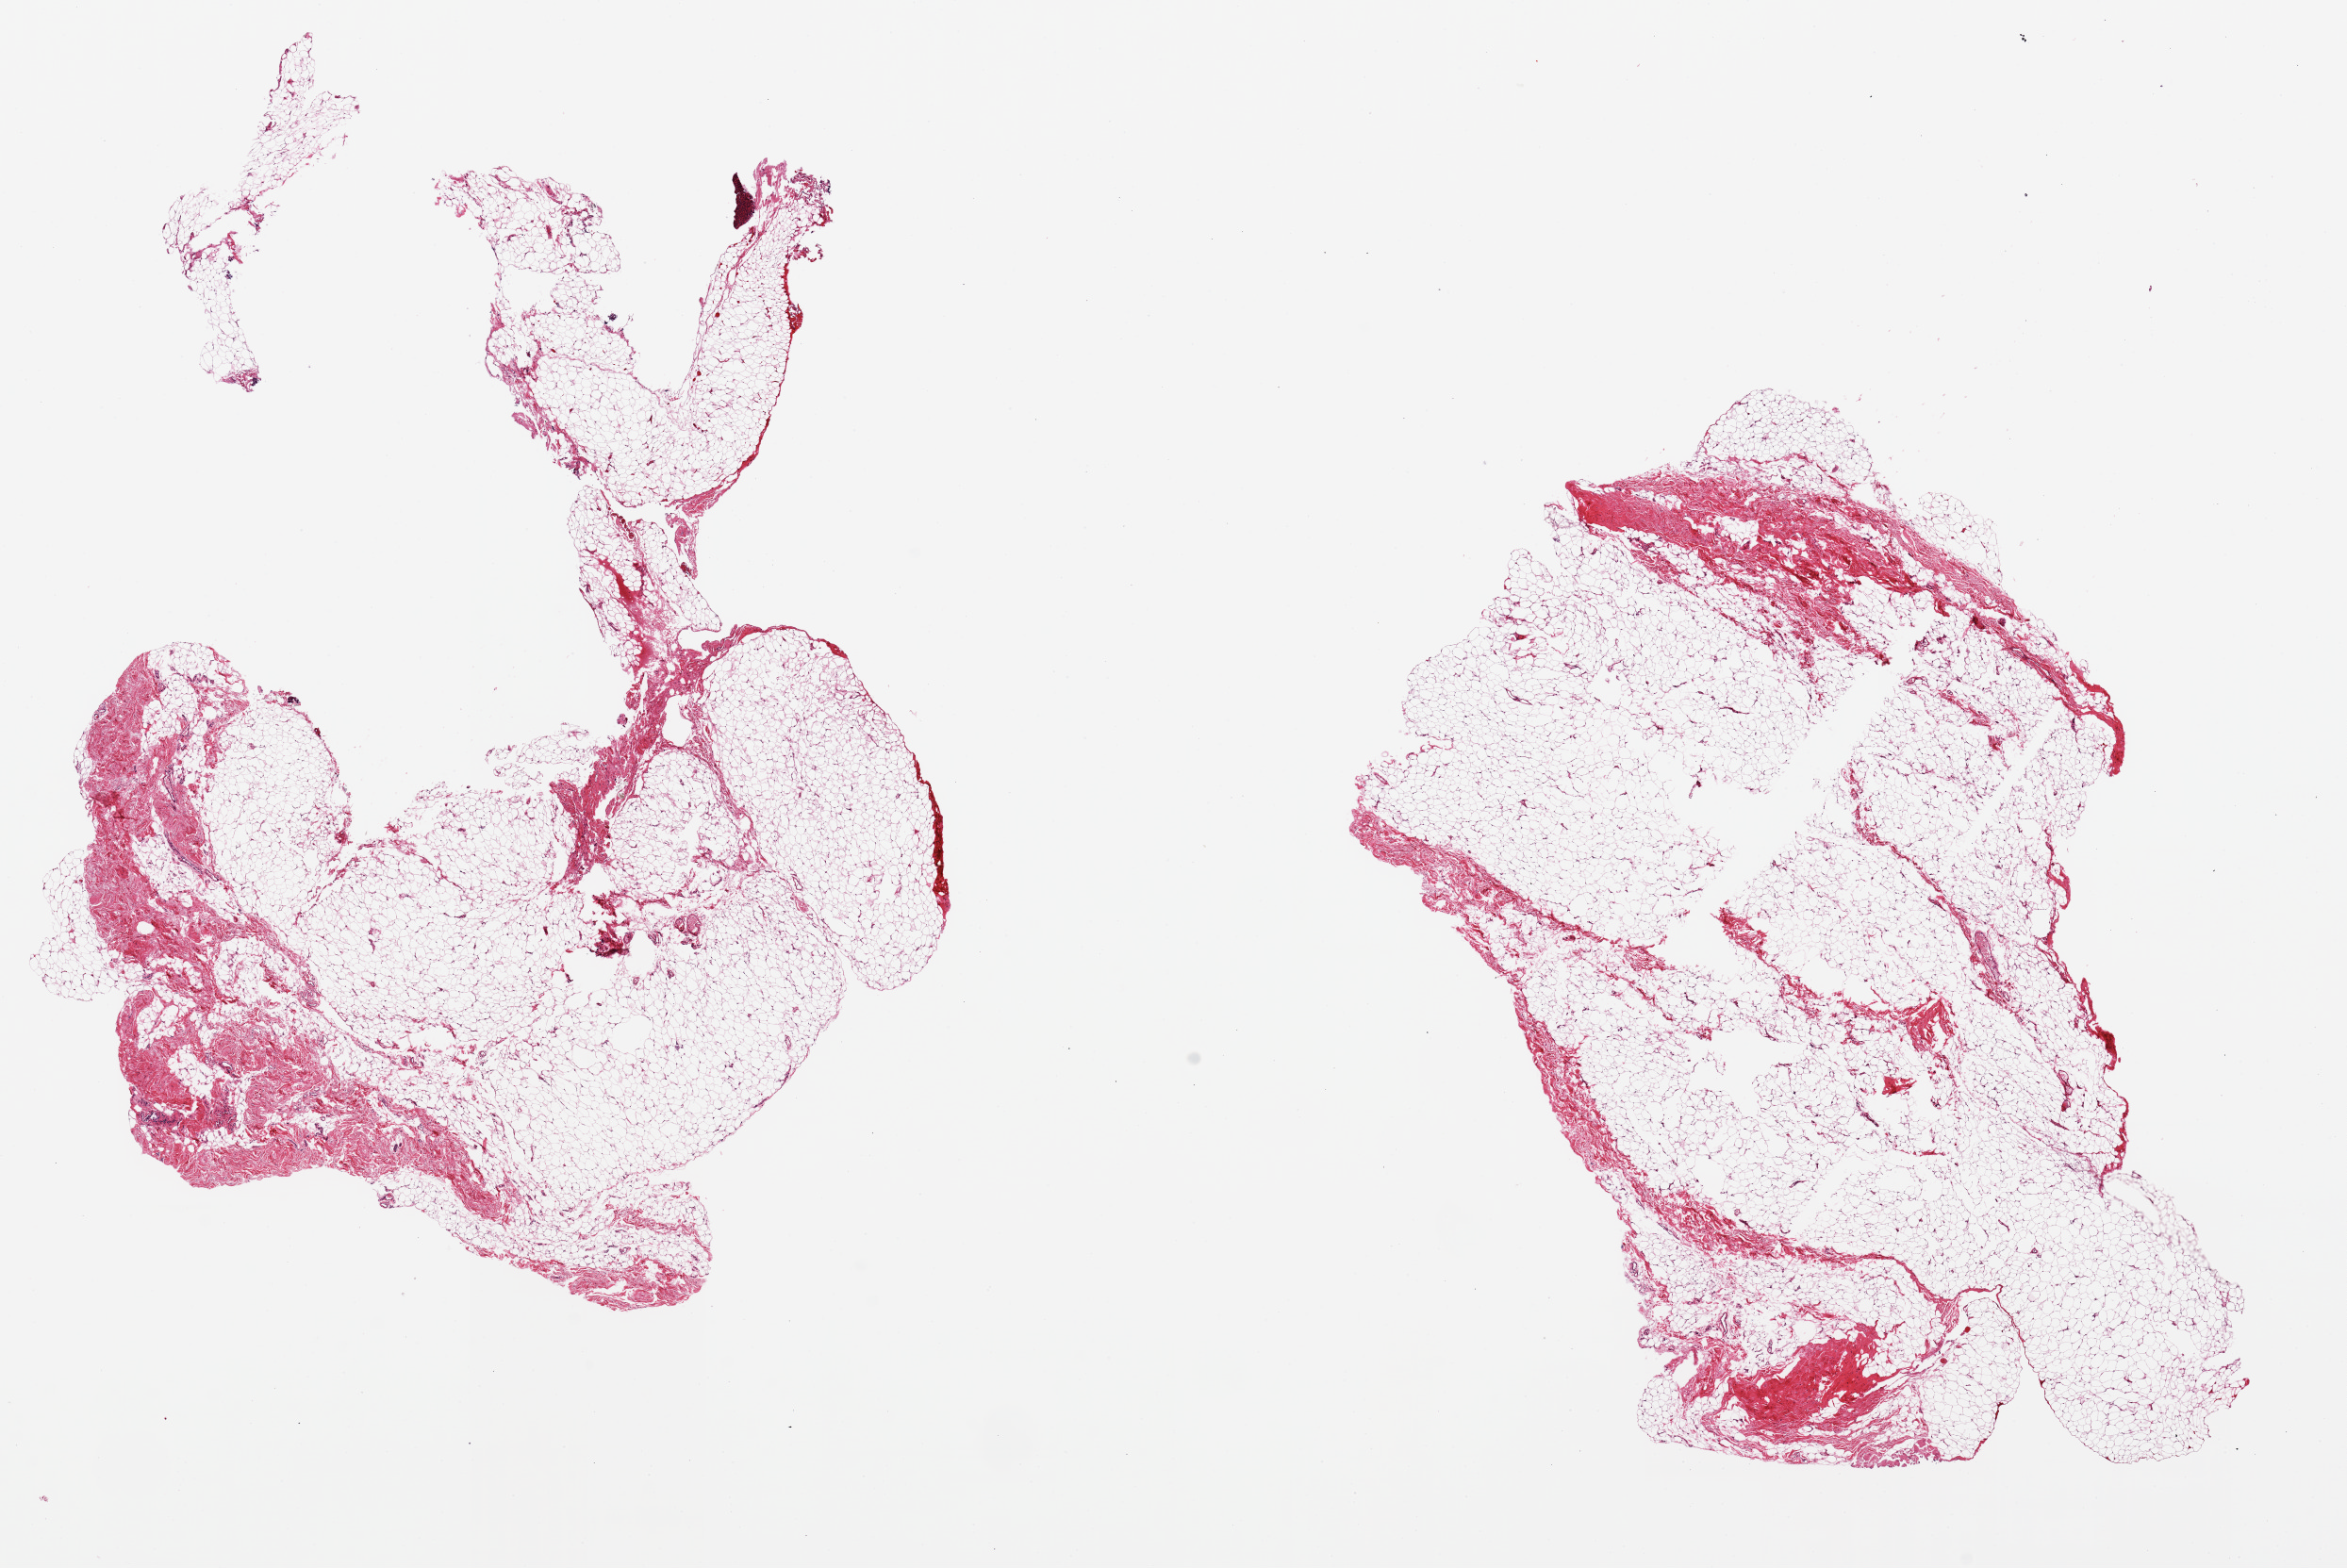
H&E whole-slide image, low-resolution overview of the scanned area, about 19.7 x 13.2 mm. PAXgene-fixed, paraffin-embedded tissue. Section of adipose tissue (target tissue). Donor tissue sample. Donor: female.
Pathologist's review note for this sample: 2 pieces, ~20% commingled fascia.